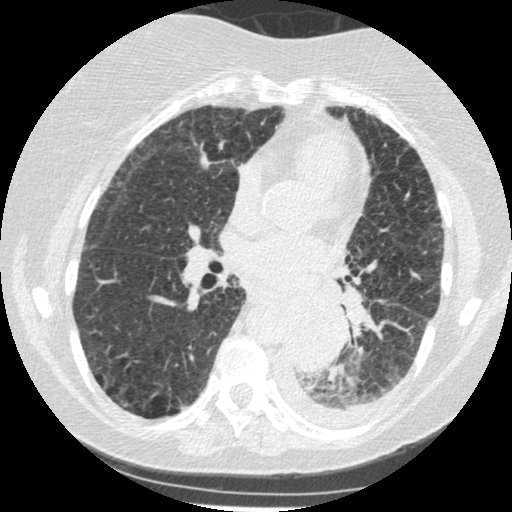
Low-dose screening chest CT, axial slice, third screening round (two years after baseline), lung window (W 1500 / L -600 HU), 1.25 mm slice thickness. Female participant, aged 60 years at enrolment. Former smoker at enrolment.
• Lesion marked by an expert reader, box from (x=274, y=305) to (x=343, y=375) px.
• Screening reader's record for this exam (one nodule recorded; not confirmed to be the boxed lesion): non-calcified nodule or mass ≥4 mm, left lower lobe, 54 × 38 mm, smooth margins, soft tissue attenuation, pre-existing on the prior screen: yes; interval growth: yes.